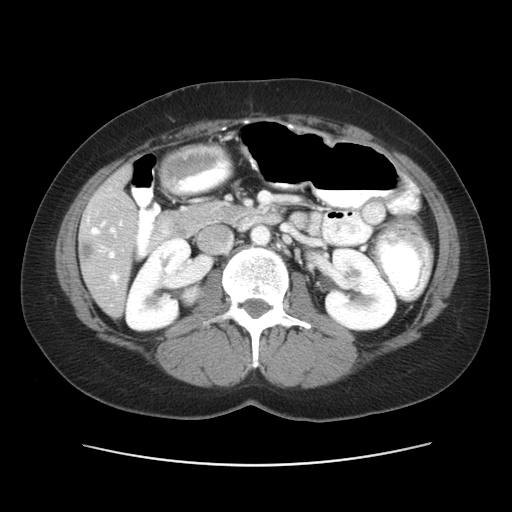
Contrast-enhanced abdominal CT, one axial slice. Position 22 of 52 along the scan axis. Reconstruction kernel STANDARD. Intravenous contrast given. Soft-tissue window (W 400 / L 40 HU). 512 × 512 image matrix, field of view 362 × 362 mm. Female patient, age 48 years. From the clinical record (not read from this slice): diagnosis: colorectal cancer liver metastases, imaged before liver resection; multiple liver metastases: yes; largest metastasis: 4.5 cm; disease in both lobes: yes.
Annotated regions visible in this slice (expert manual segmentation):
- hepatic veins: bounding box [x1, y1, x2, y2] px = [91, 222, 121, 282]
- liver: [79, 170, 140, 315]
- portal vein (with intrahepatic branches): [102, 222, 115, 258]
- liver metastasis: [84, 242, 96, 260]